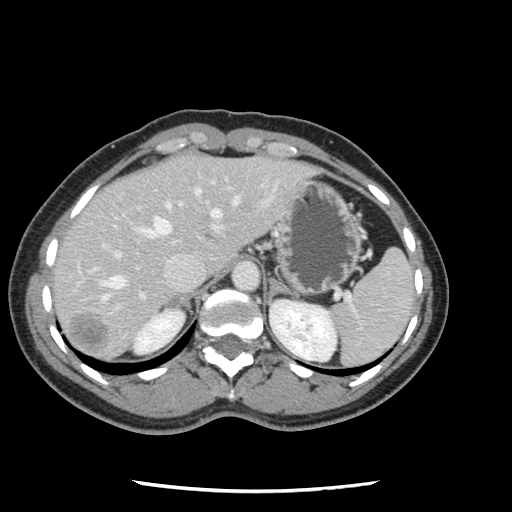
Contrast-enhanced abdominal CT, one axial slice; 120 kVp; intravenous contrast given; soft-tissue window (W 400 / L 40 HU); 2.5 mm slice thickness; 512 × 512 image matrix. Female patient, age 43 years. From the clinical record (not read from this slice): diagnosis: colorectal cancer liver metastases, imaged before liver resection; multiple liver metastases: yes; largest metastasis: 3.4 cm; disease in both lobes: yes.
Outlined on this slice (expert manual segmentation):
- hepatic veins: bounding box <101,188,239,301> (left, top, right, bottom; pixels)
- liver: <54,155,312,361>
- planned liver remnant (the part of the liver to remain after resection): <54,159,191,309>
- portal vein (with intrahepatic branches): <69,180,230,315>
- liver metastasis: <71,314,110,351>